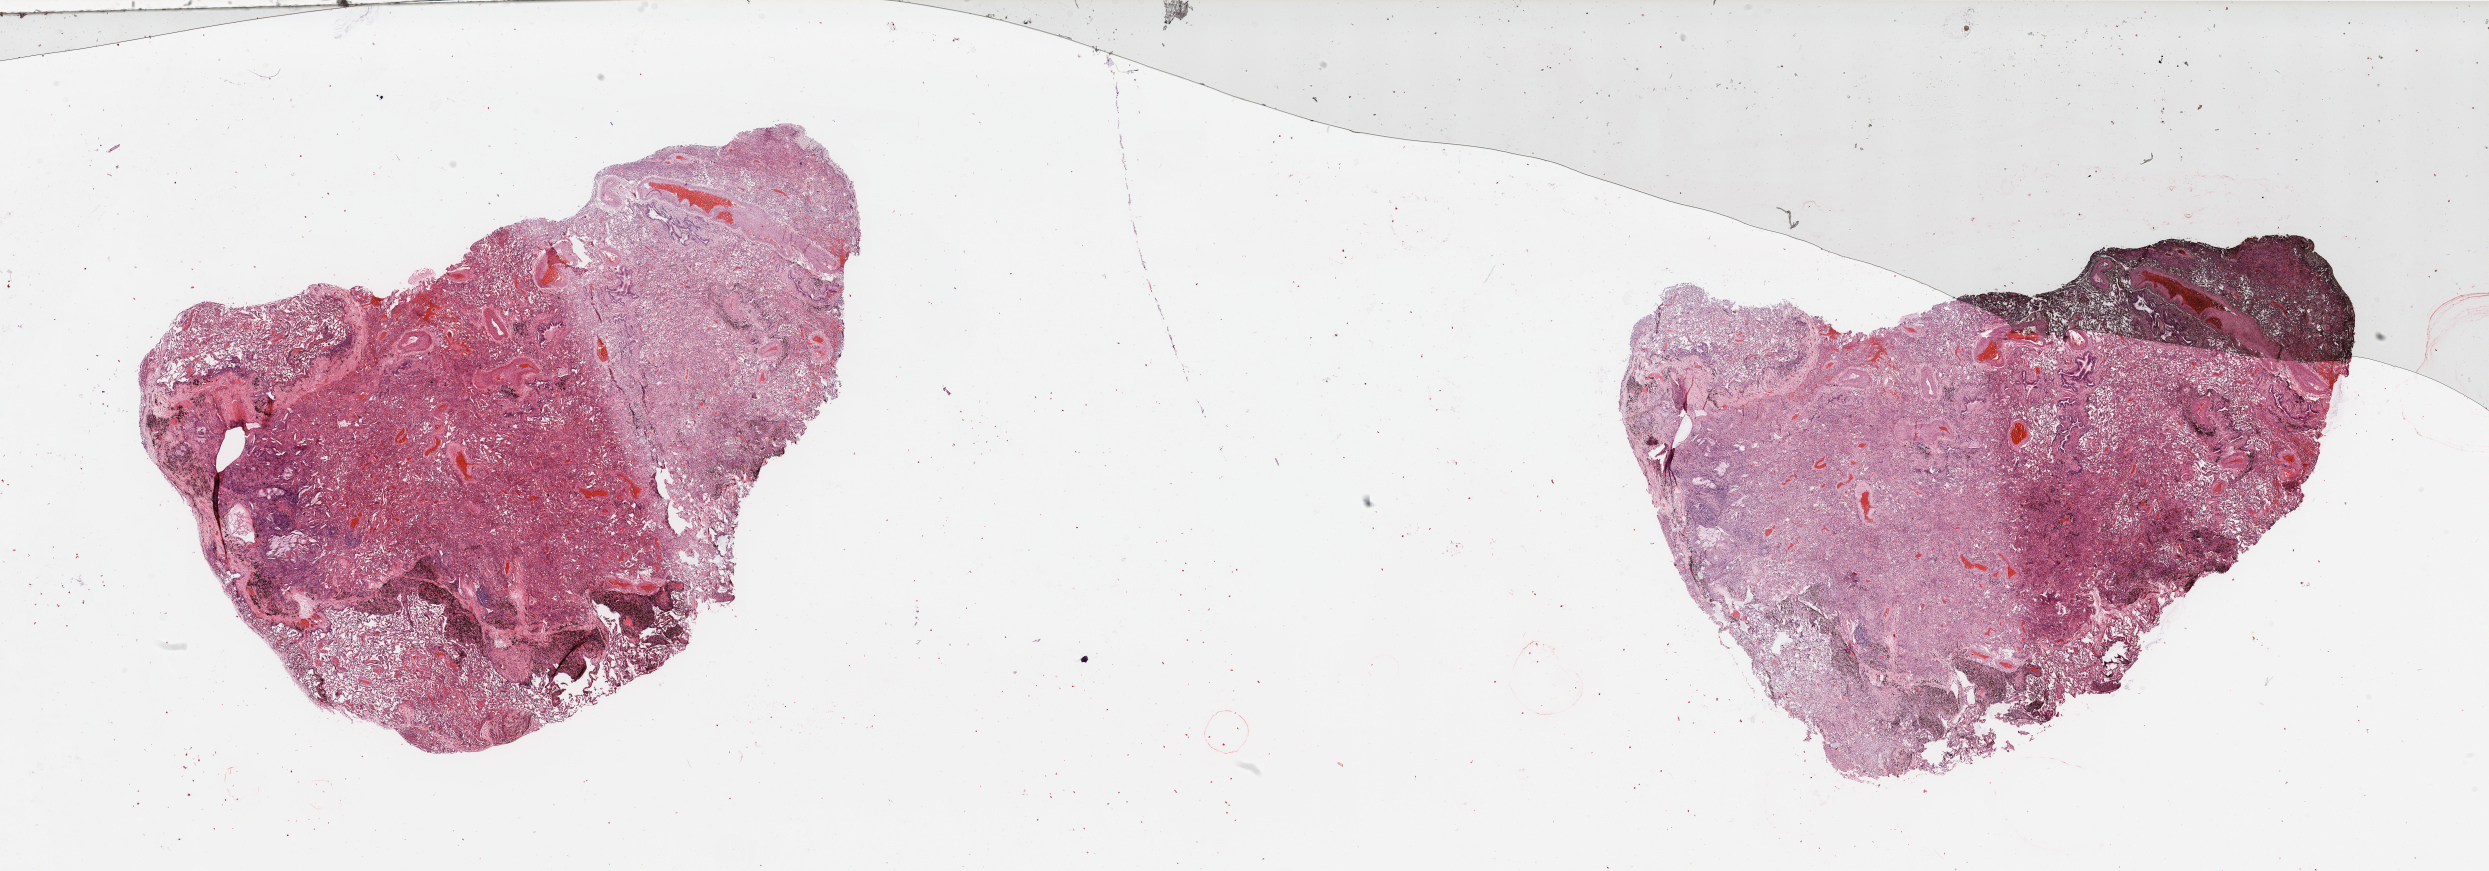
Digitized H&E-stained tissue section (whole slide), a low-resolution overview of the entire scanned area, about 39.4 x 13.8 mm, normal (non-tumour) tissue sample, lung. Patient: male, age 65 years.
This section: normal (non-tumour) tissue from the same patient. Patient diagnosis: Squamous cell carcinoma, NOS.